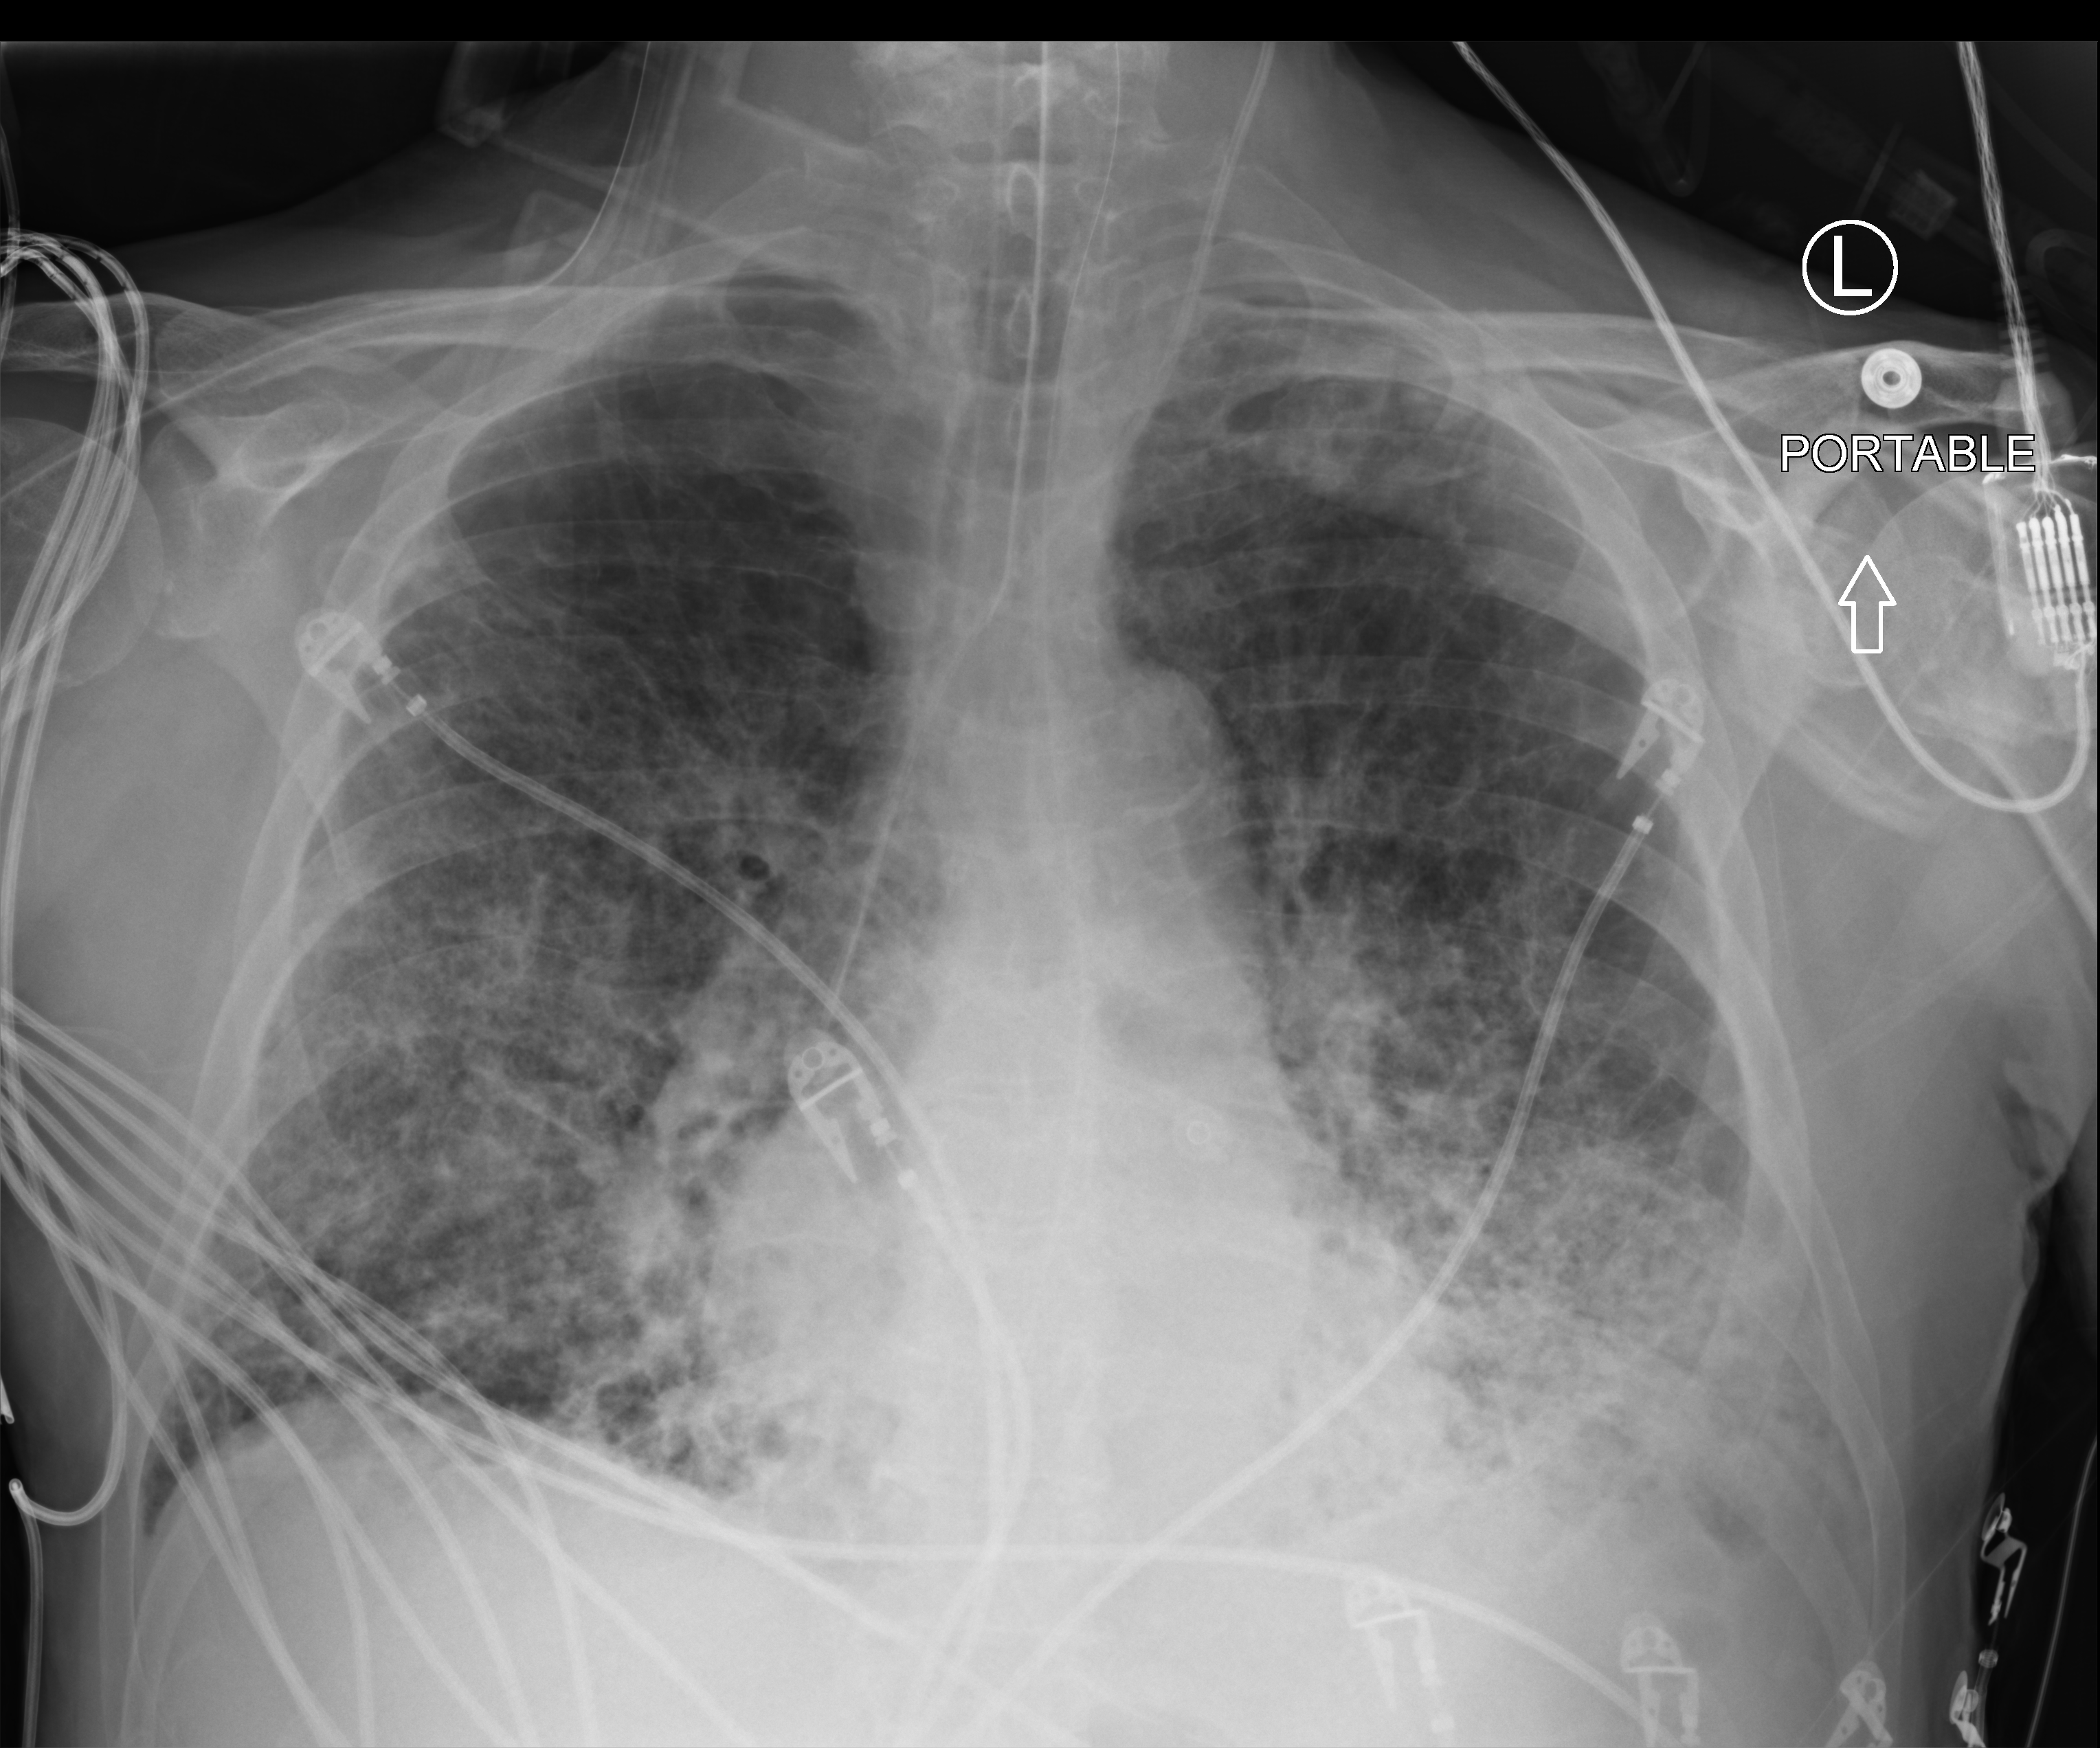
Bedside chest radiograph (computed radiography), anteroposterior (AP) projection. Patient hospitalised with COVID-19; male, aged 75–90 years.
From the hospital-stay record, not from the radiograph (when in the stay this image was taken is not recorded): smoking status (admission record): never; chronic kidney disease (admission record): no.